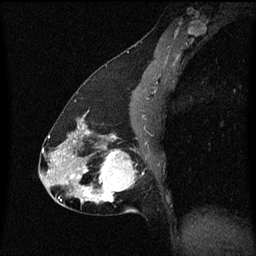
Breast MRI (dynamic contrast-enhanced), one sagittal slice; slice 30 of 60 in the series (ordered by position); dynamic contrast-enhanced series, image 2 of 3 at this slice position (ordered by acquisition); 1.5 T; TE 4.2 ms, TR 8.4 ms; 2 mm slice thickness; 256 × 256 image matrix, field of view 200 × 200 mm. Patient: female, 47 years.
Annotated regions visible in this slice (semi-automatic segmentation, software-assisted and operator-edited):
- analysis volume of interest (the breast-tissue region the enhancement analysis was run in; not a lesion): box from (x=81, y=138) to (x=139, y=213) px
- tumour enhancement mask (voxels above the 70 % enhancement threshold inside the analysis volume of interest): (x=81, y=138)–(x=135, y=203)